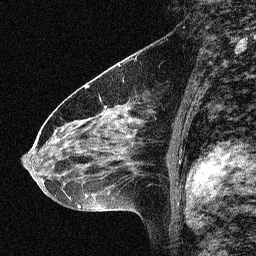
Breast MRI (dynamic contrast-enhanced), one sagittal slice. Position 36 of 64 along the scan axis. Dynamic contrast-enhanced study with each time point stored as its own series, time point 2 of 3 at this slice position (early post-contrast, ordered by acquisition time). 1.5 T. TE 4.5 ms, TR 11 ms. 2.06 mm slice thickness. 256 × 256 image matrix, field of view 200 × 200 mm. Female patient, age 46 years. Case-level facts recorded for this patient, not image findings: setting: breast cancer imaged before/during neoadjuvant chemotherapy; receptor status: HER2-positive.
Structures marked on this image (semi-automatically segmented with operator editing):
- analysis volume of interest (the breast-tissue region the enhancement analysis was run in; not a lesion): bounding box [x1, y1, x2, y2] px = [42, 80, 150, 180]
- tumour enhancement mask (voxels above the 90 % enhancement threshold inside the analysis volume of interest): [46, 105, 106, 172]